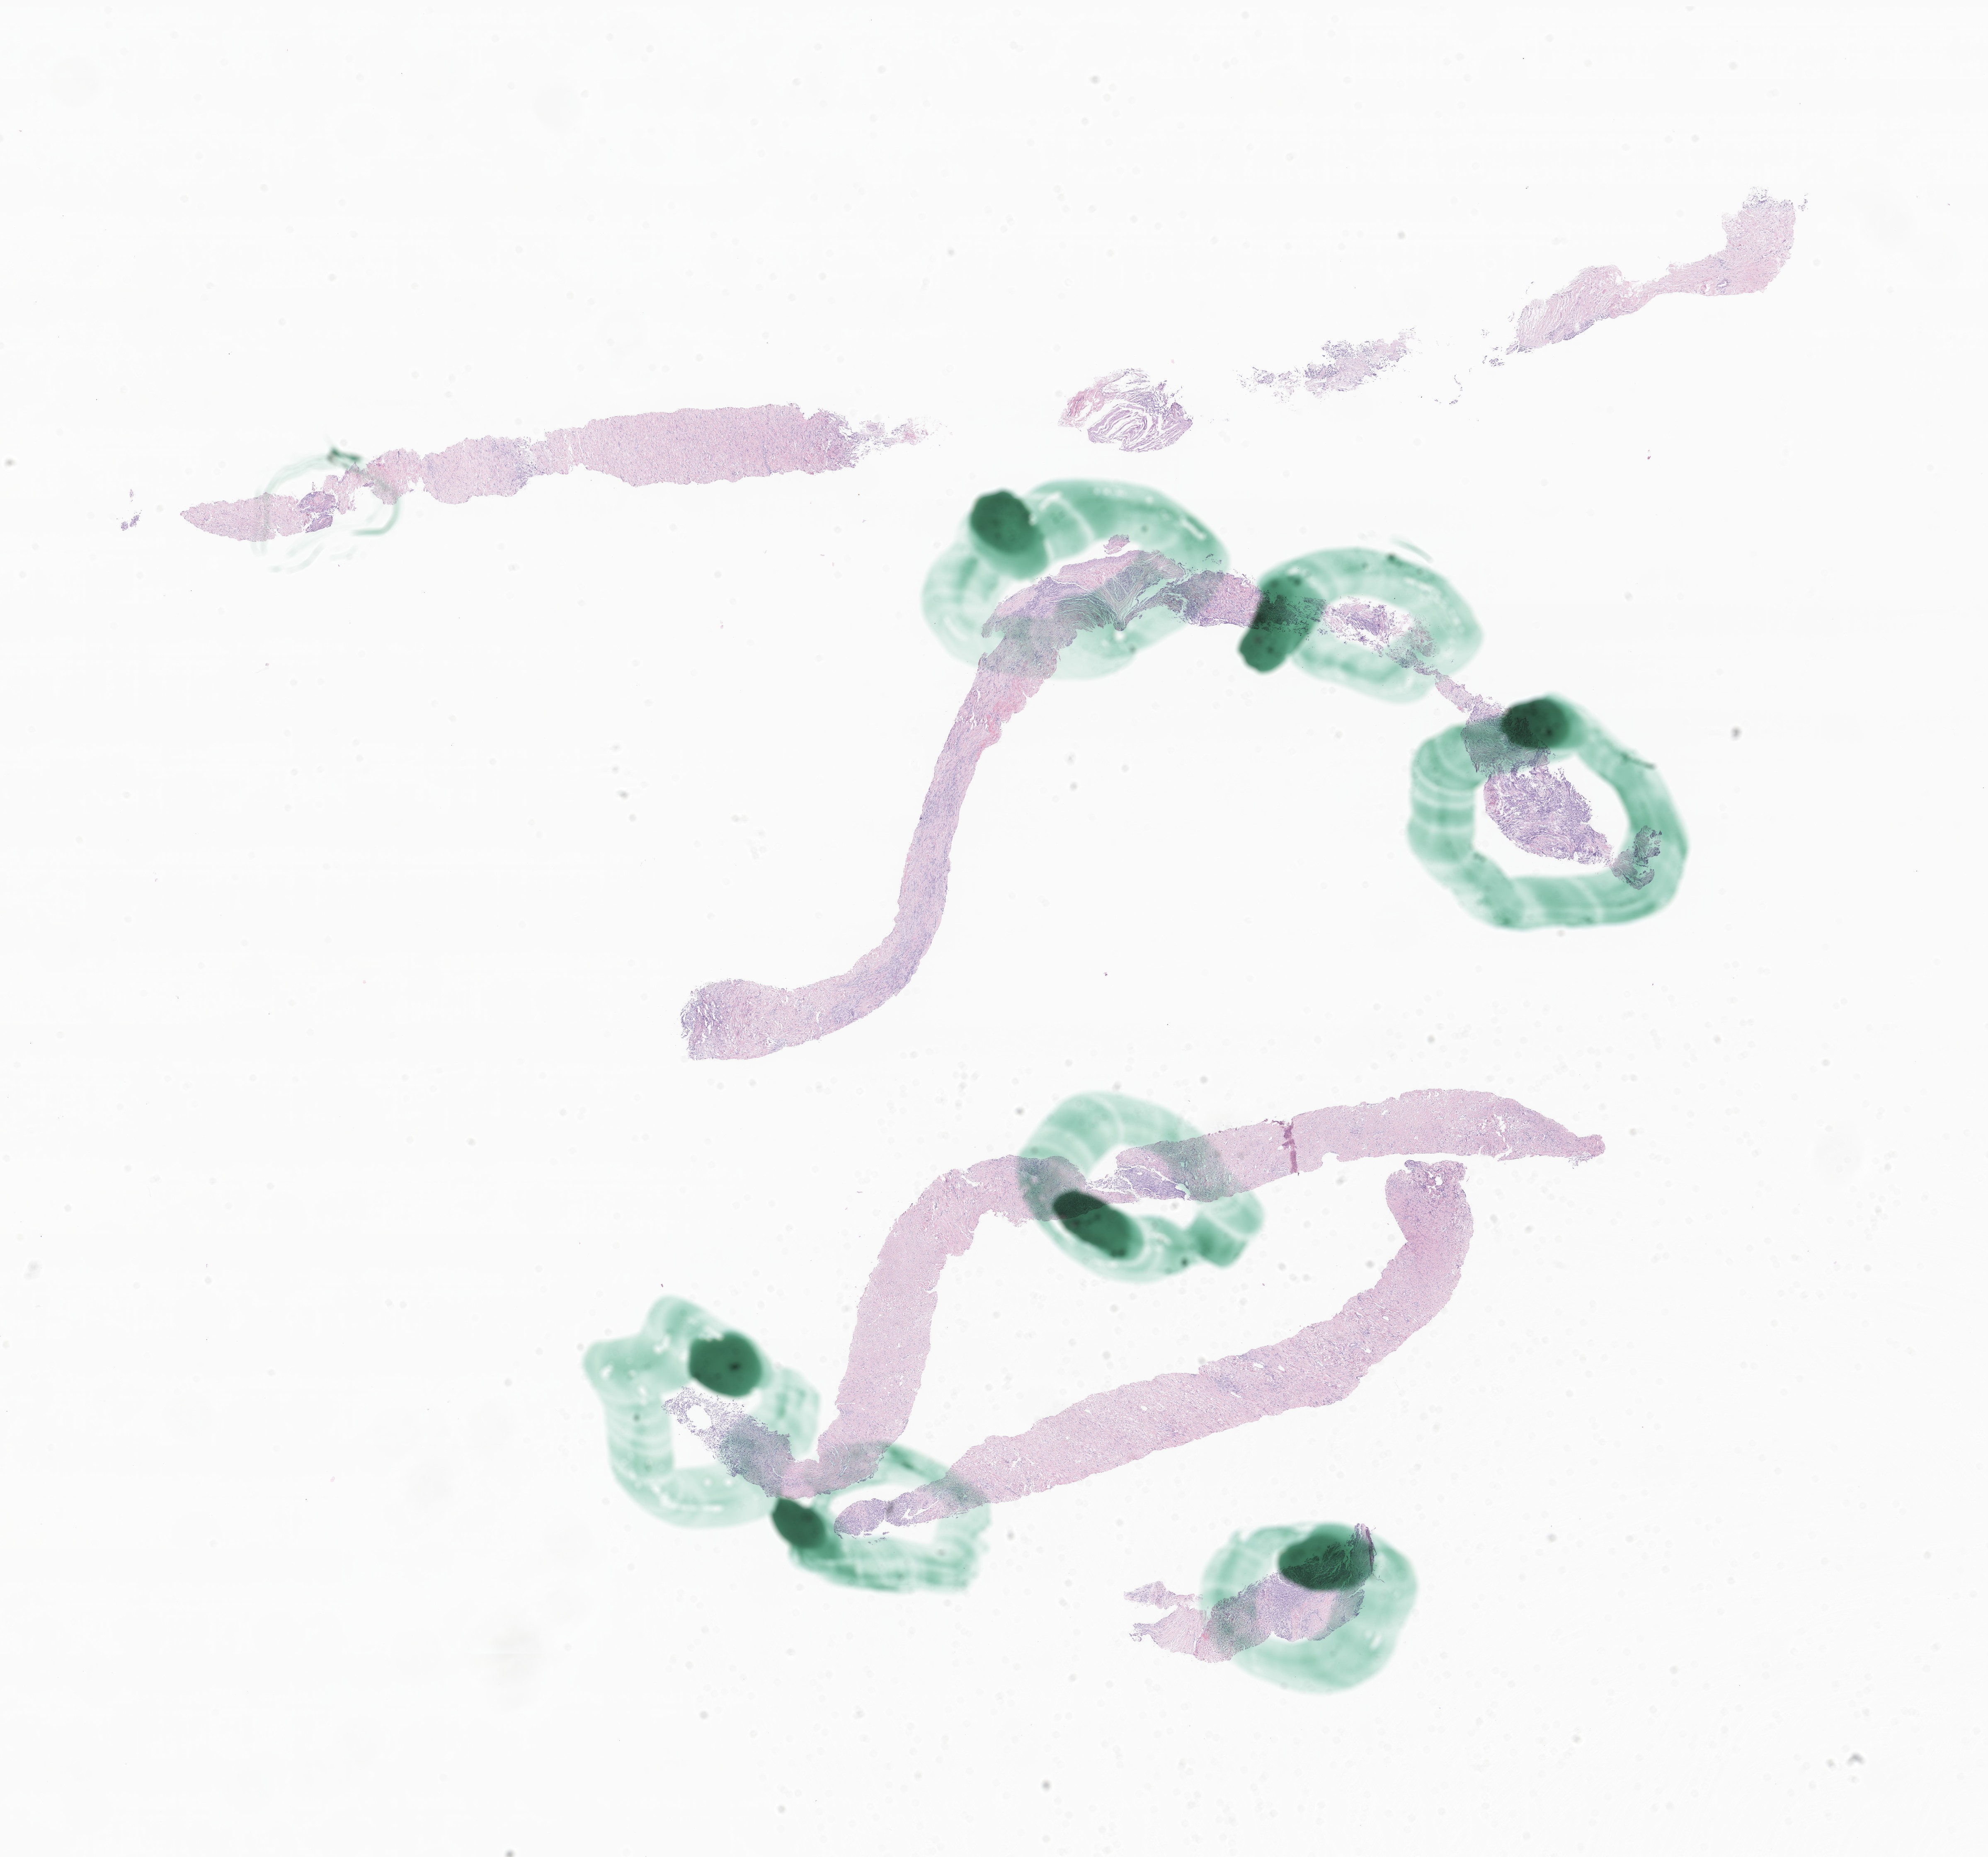
Whole-slide image, hematoxylin and eosin (H&E) stain of tumor tissue from the thorax, a low-resolution overview of the entire scanned area, about 20.2 x 18.9 mm; formalin-fixed paraffin-embedded section. Patient male; age 162 months (13 years 6 months).
Diagnosis: Synovial sarcoma, NOS.